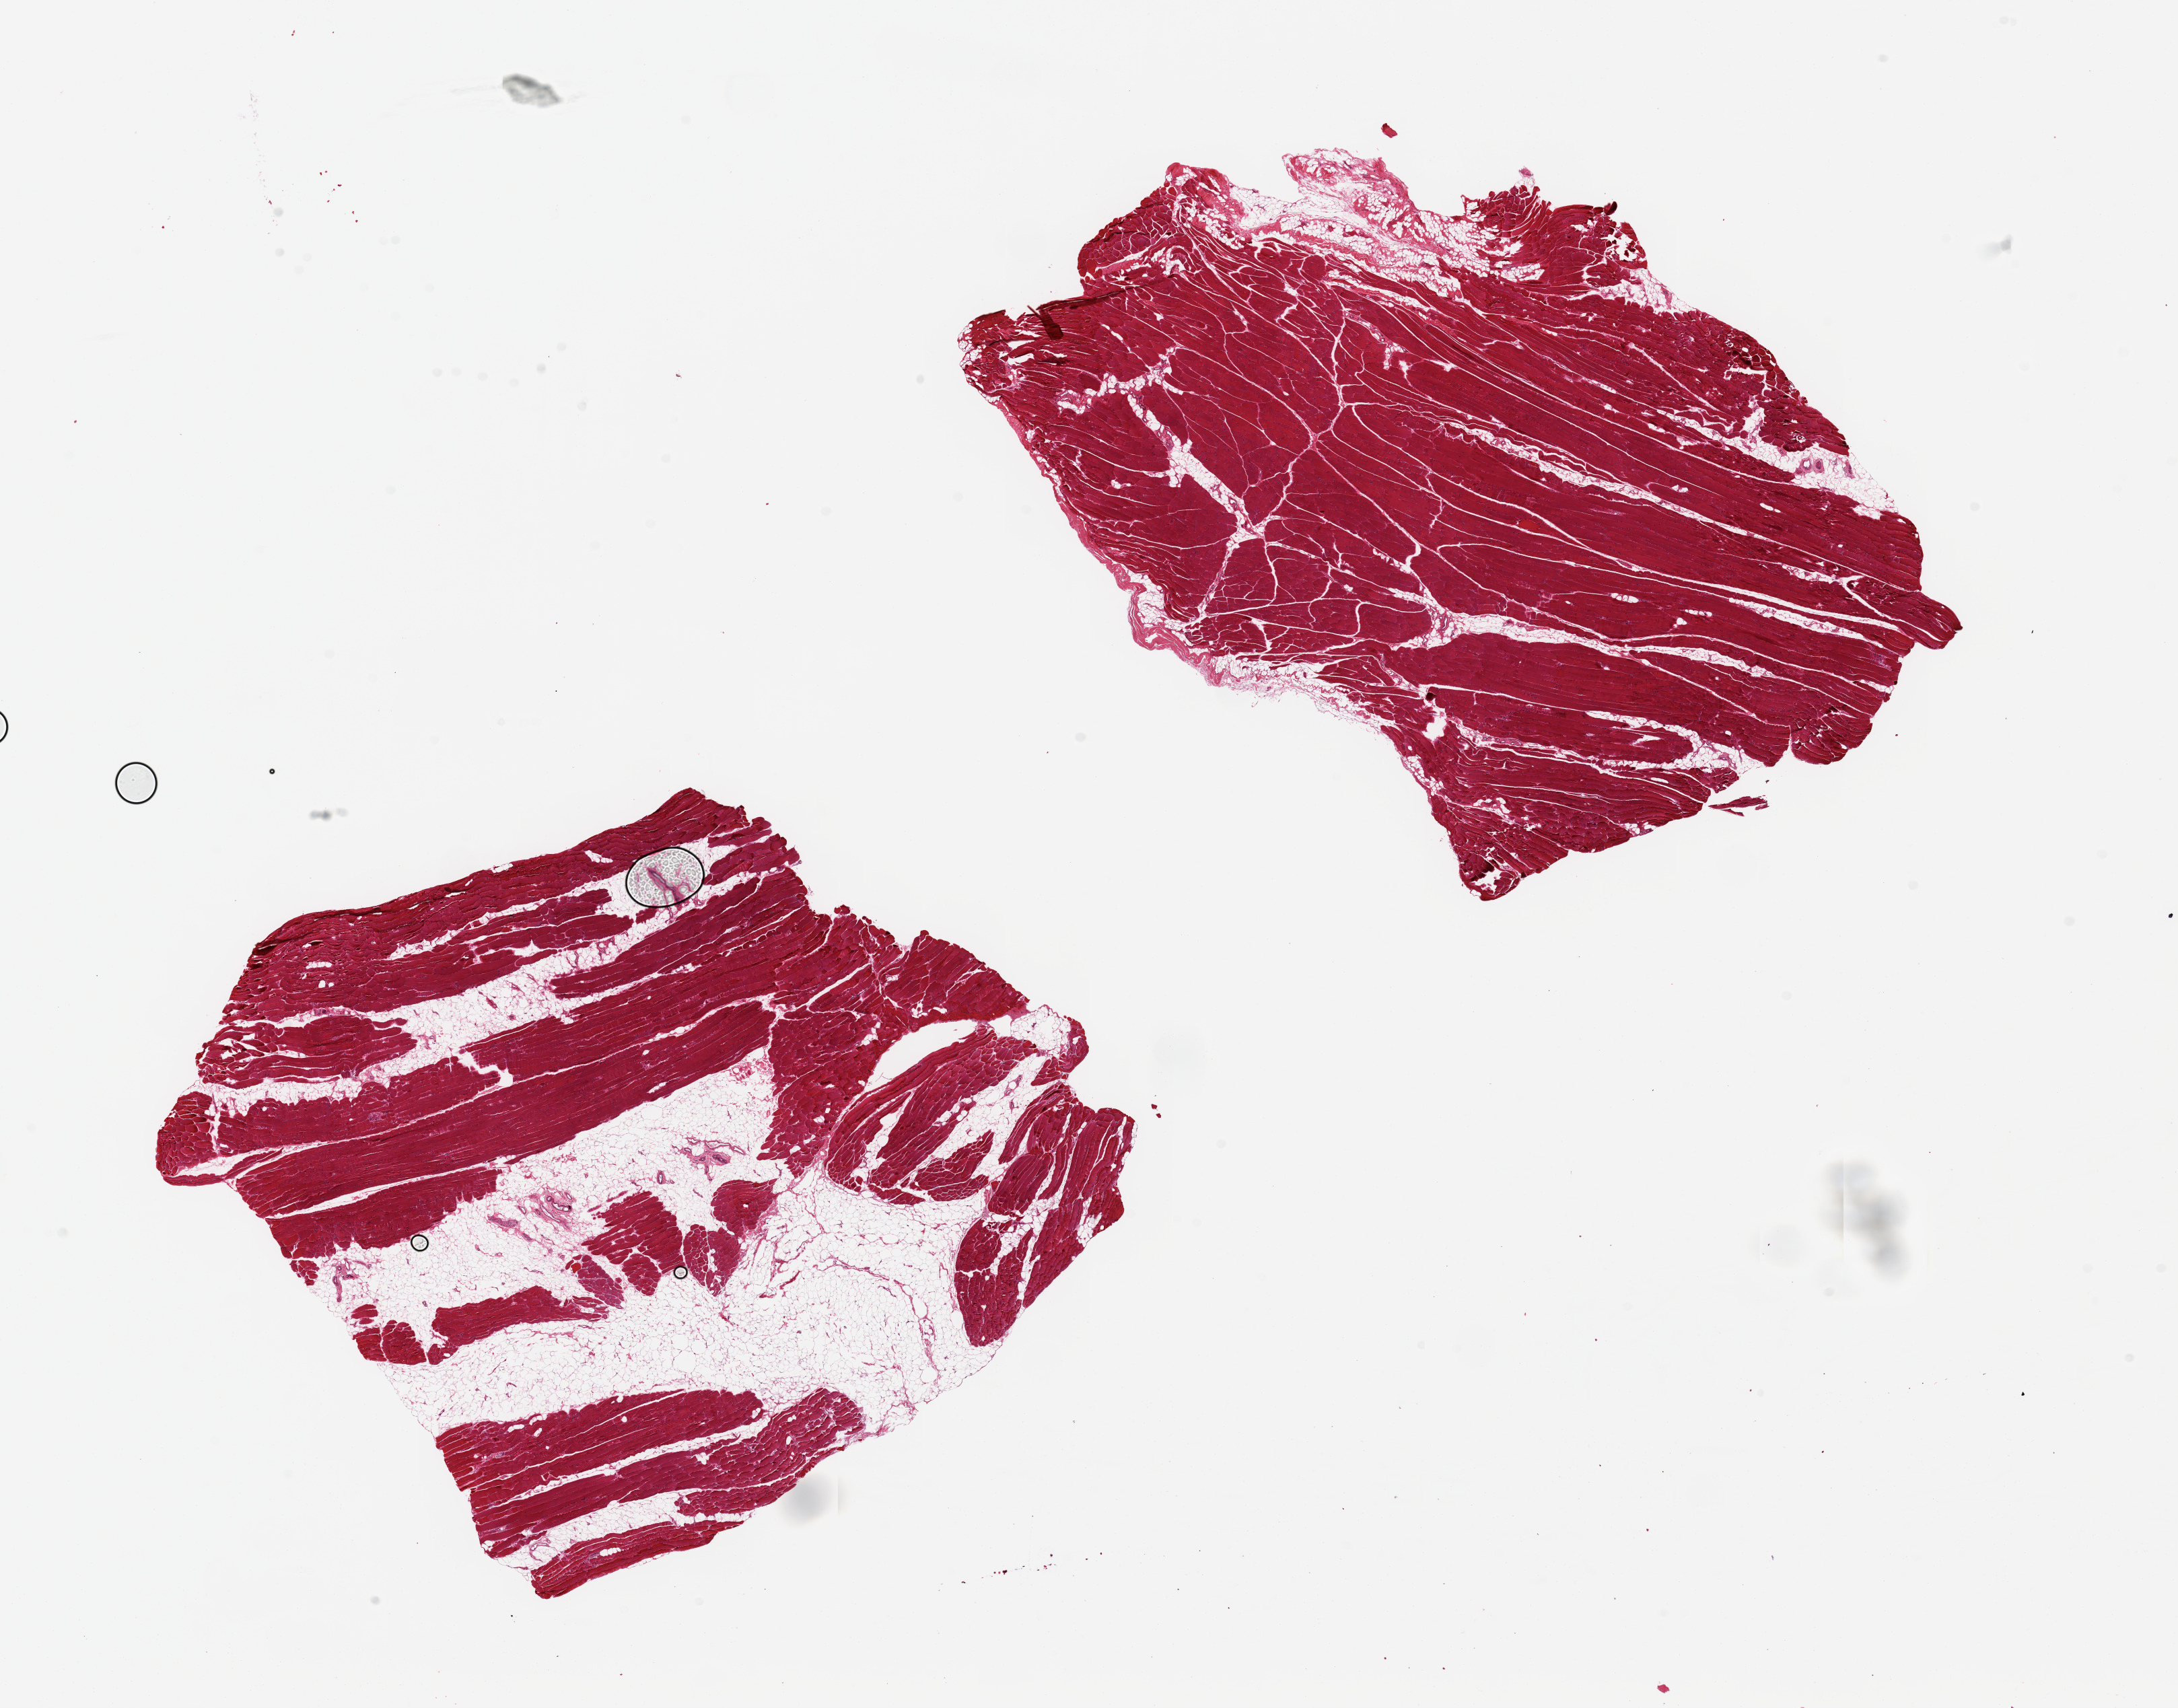
Whole-slide image, haematoxylin and eosin stain — a low-resolution overview of the entire scanned area, about 25.6 x 20.1 mm (from a 20x scan). PAXgene-fixed paraffin-embedded (PFPE) section. Sampled site (target tissue): skeletal muscle. Tissue donor sample. Donor: male.
* pathologist's review note for this sample: 2 pieces ~8x7 mm, 10-20% interstitial fat/fibrous tissue